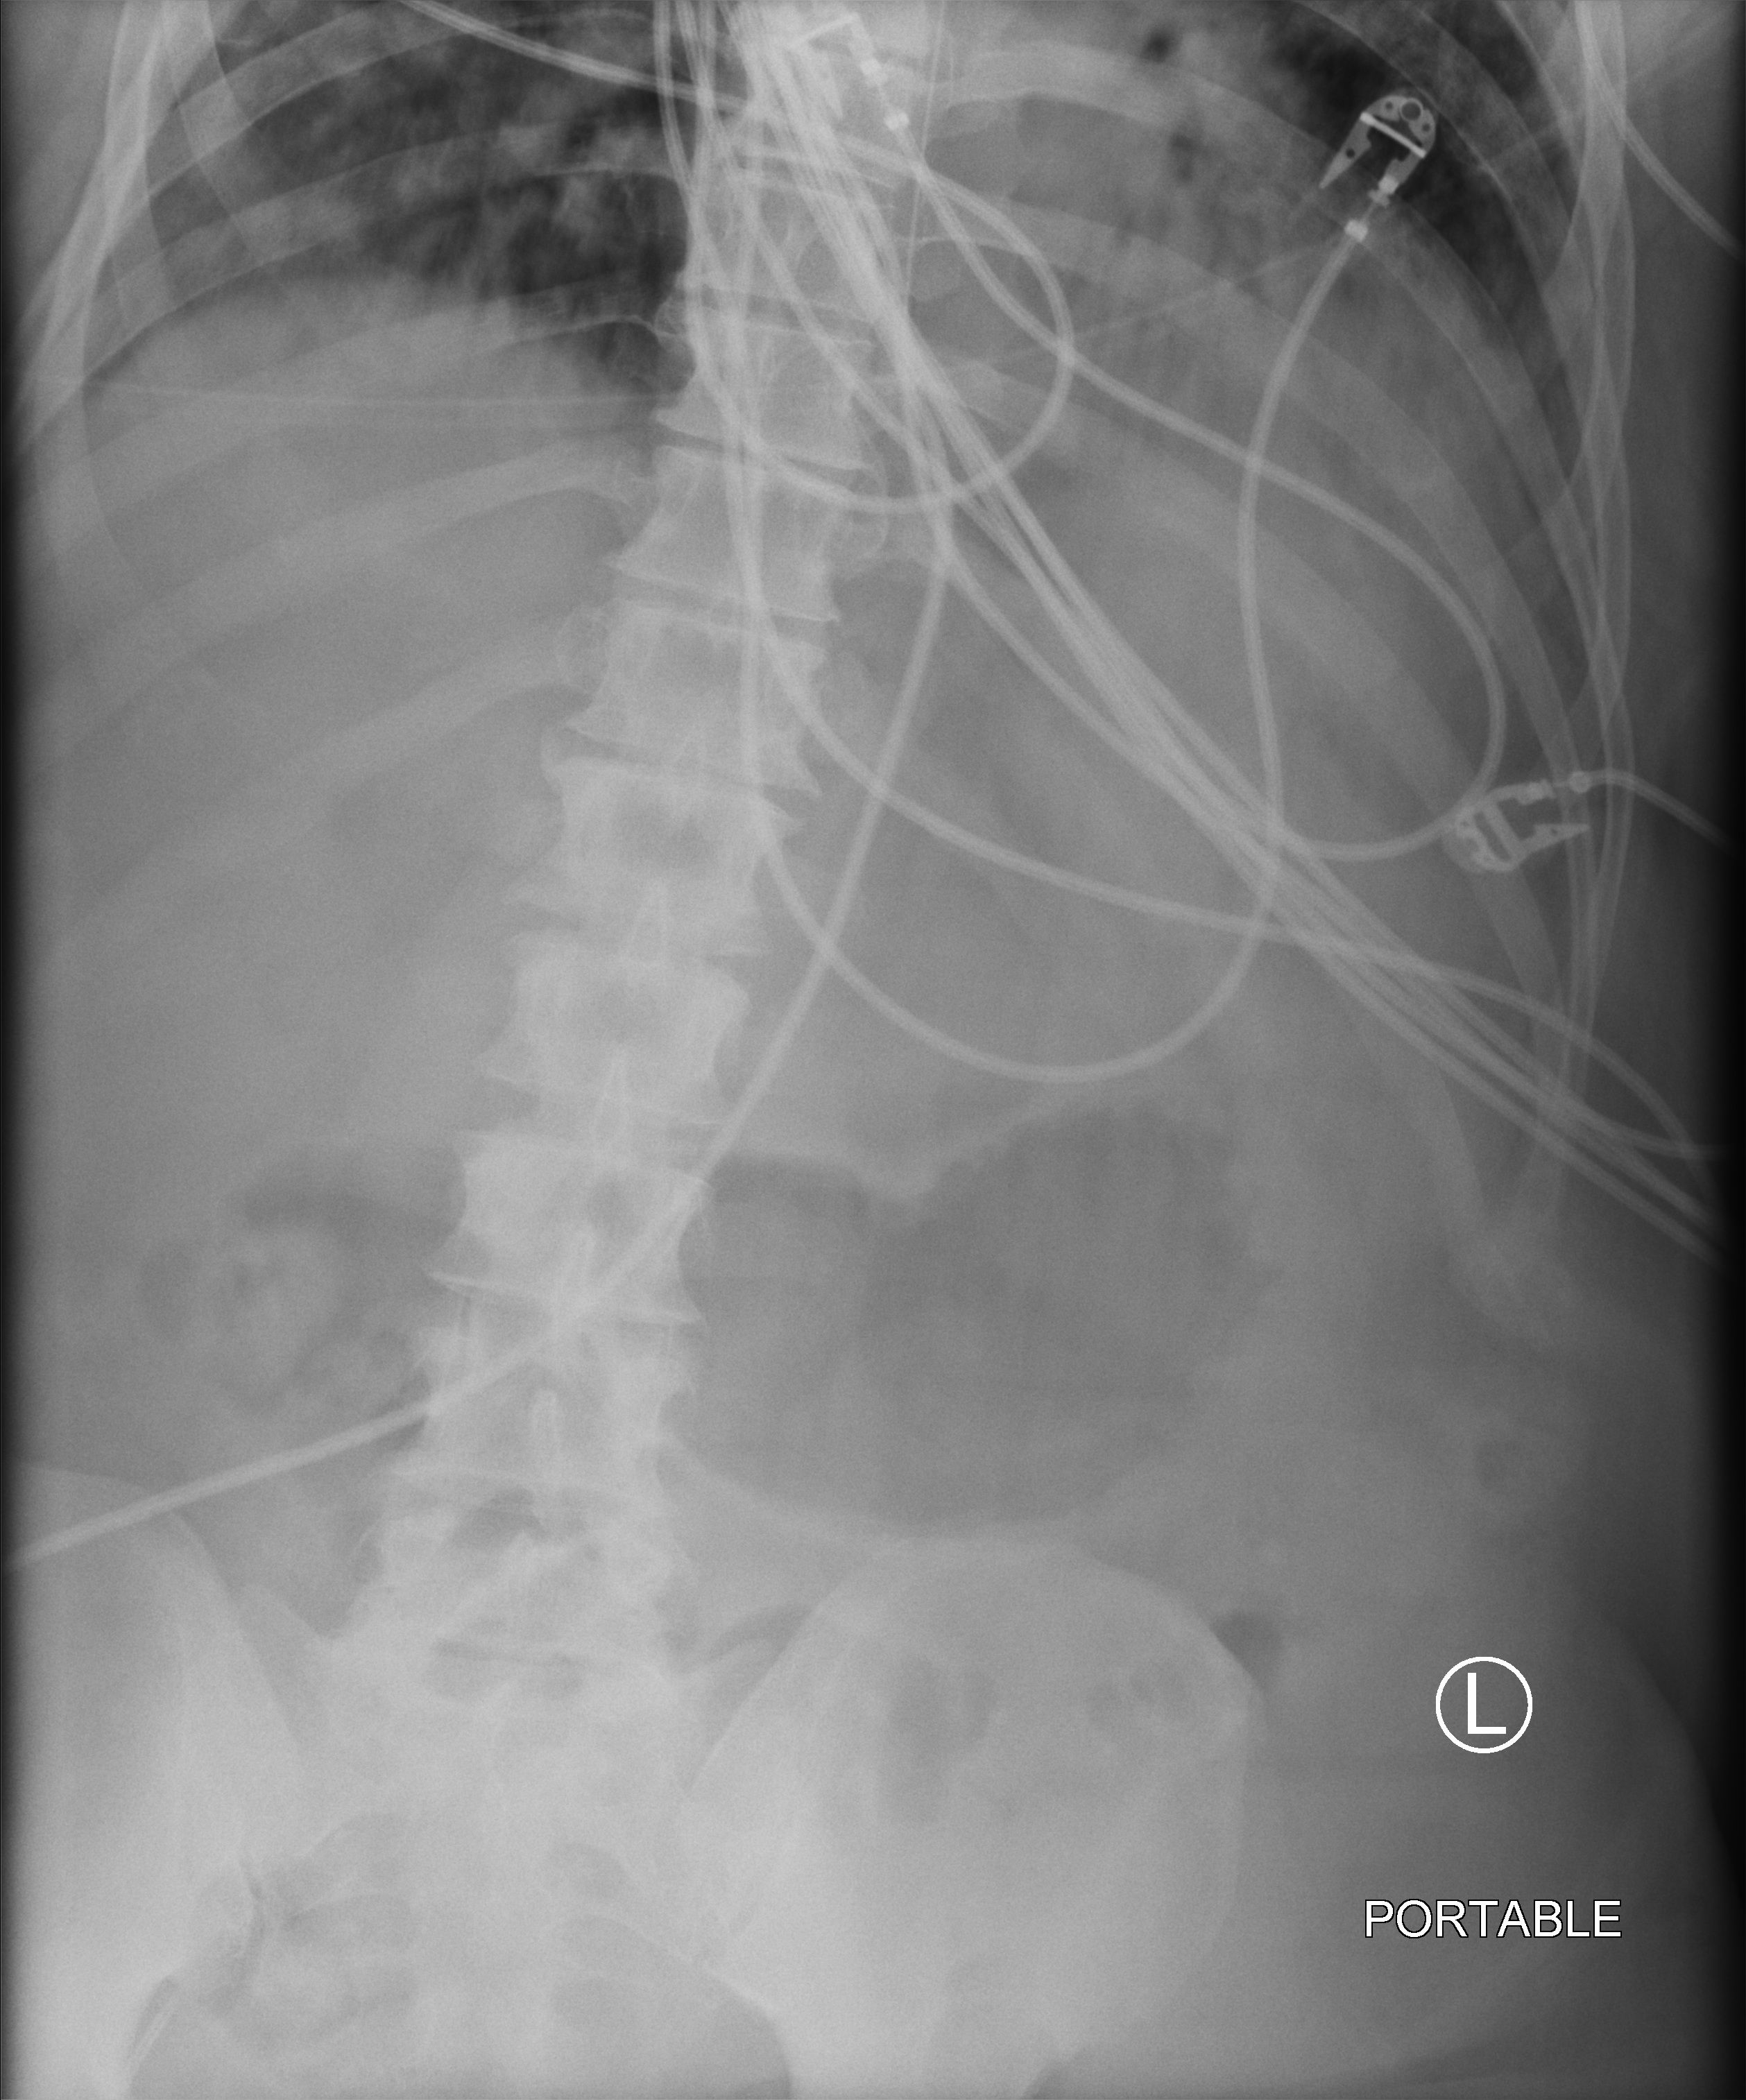
Abdomen X-ray (portable); anteroposterior (AP) projection. Male patient hospitalised with COVID-19, age 60–74 years.
Hospital-stay facts (about this admission, not read from this image; timing relative to this image not recorded):
- length of hospital stay: 40 days